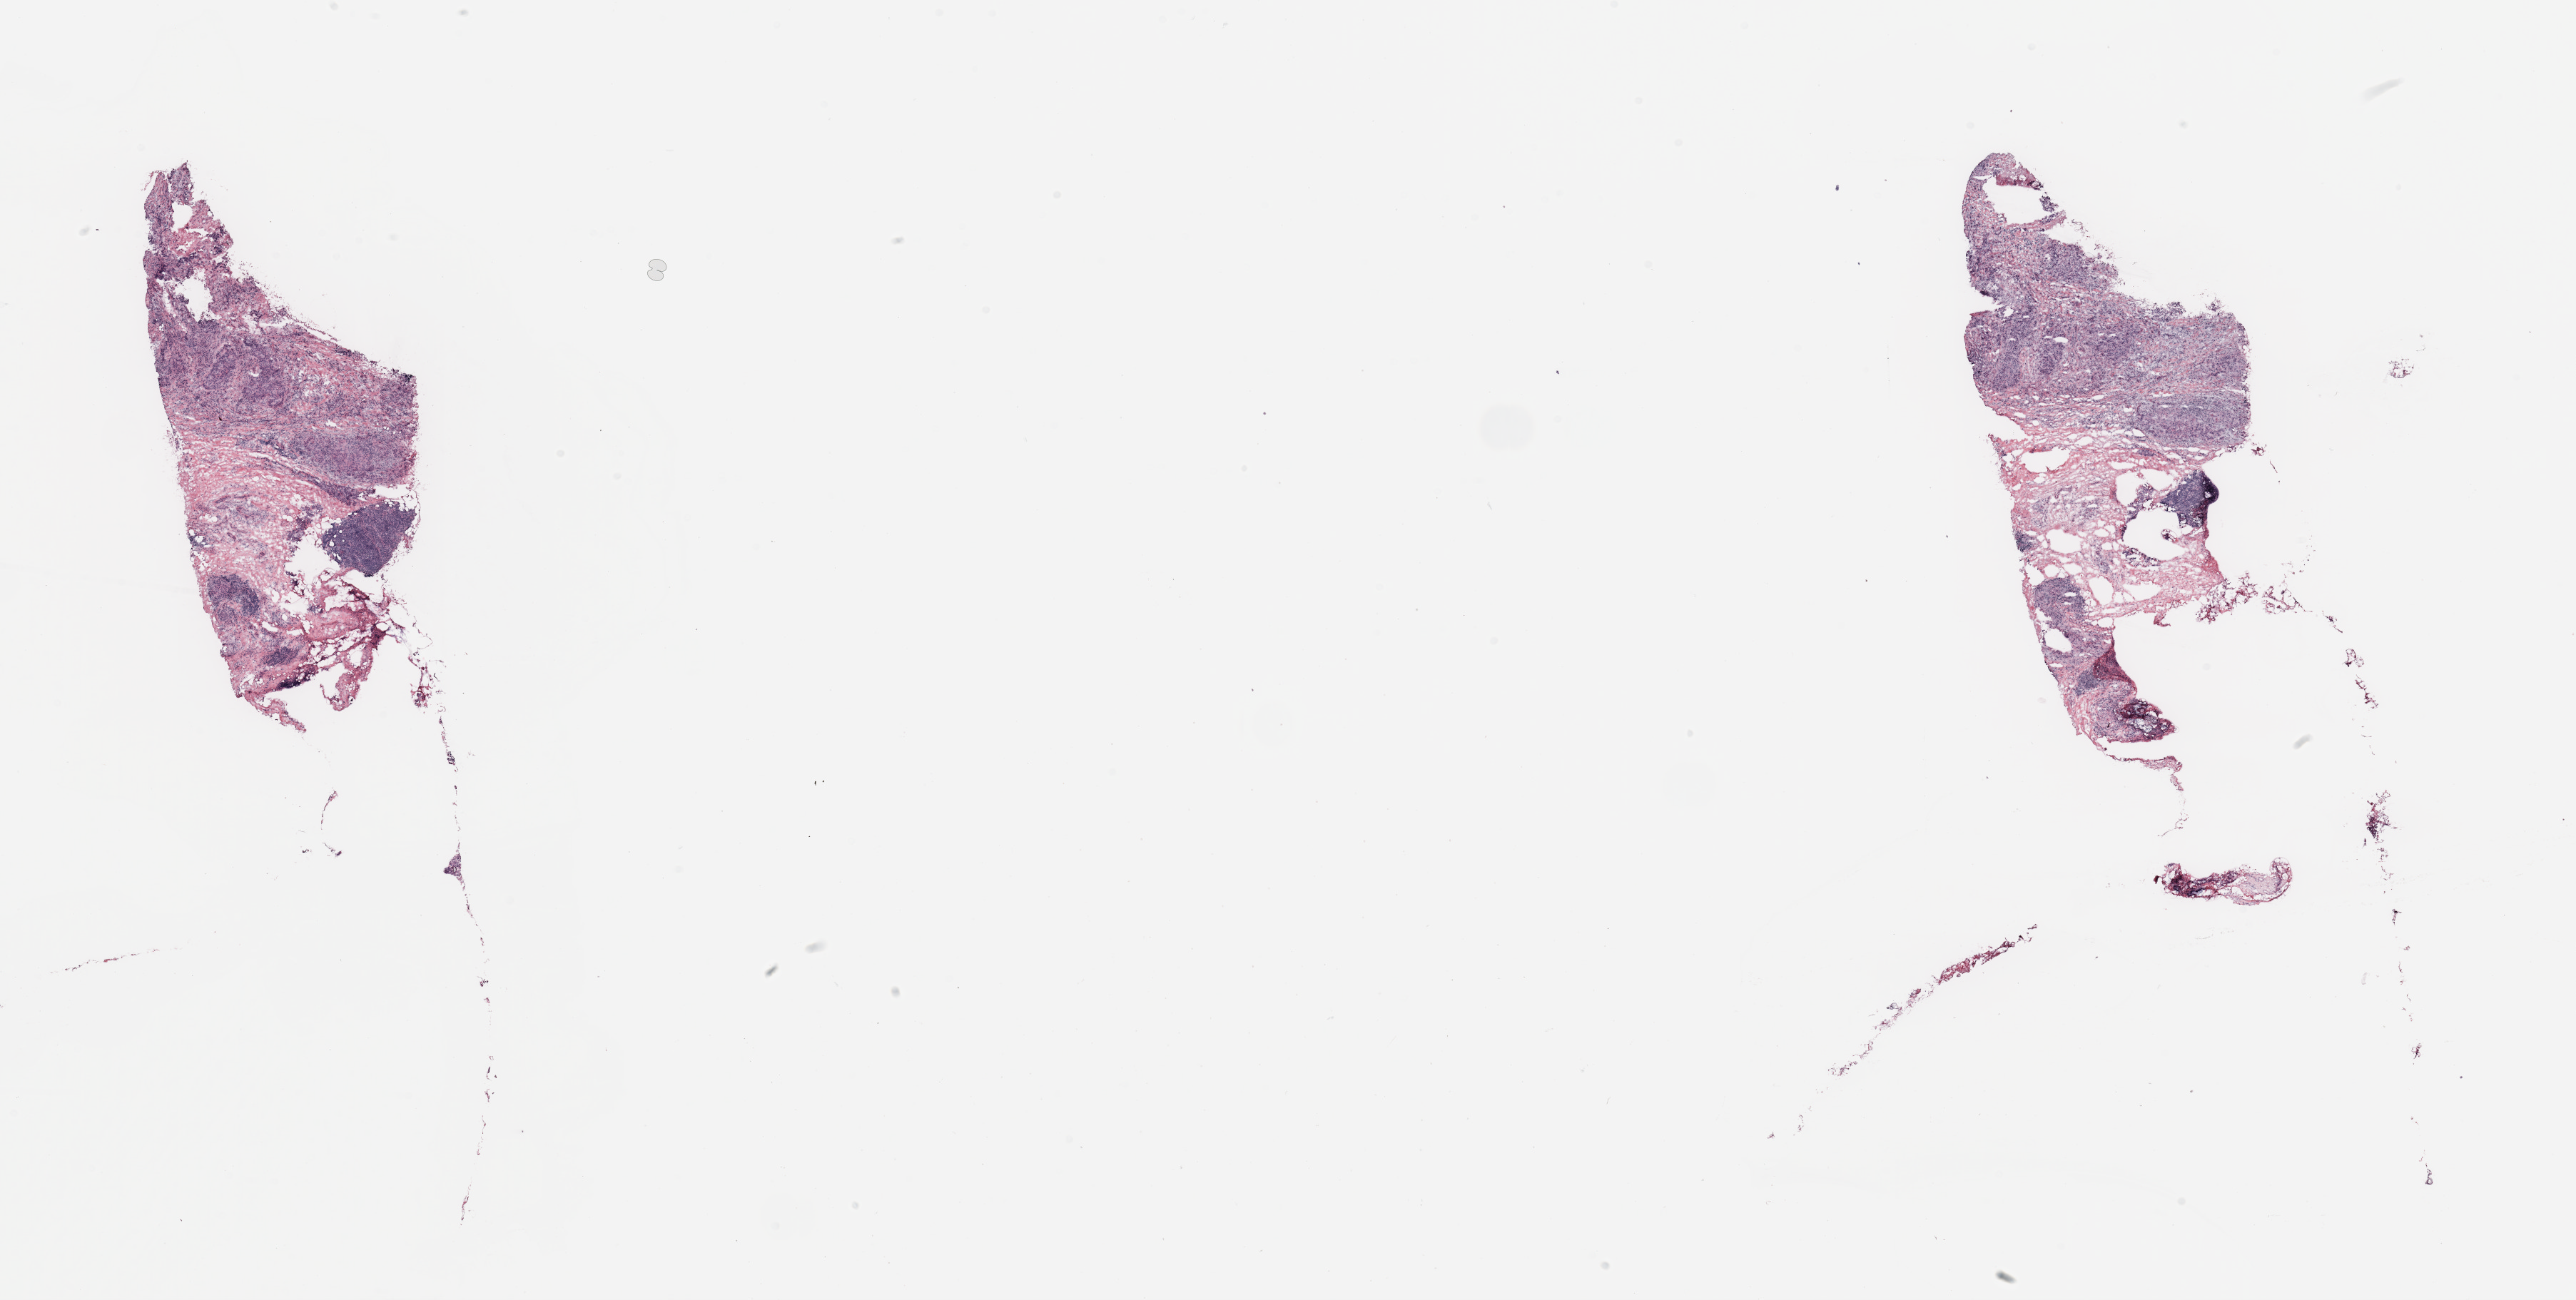
H&E-stained whole-slide image — shown as a low-resolution overview of the whole scanned area (about 28.5 x 14.4 mm, slide scanned at 20x). Breast, tissue type not recorded.
• patient diagnosis (cohort enrolment): breast cancer (breast)